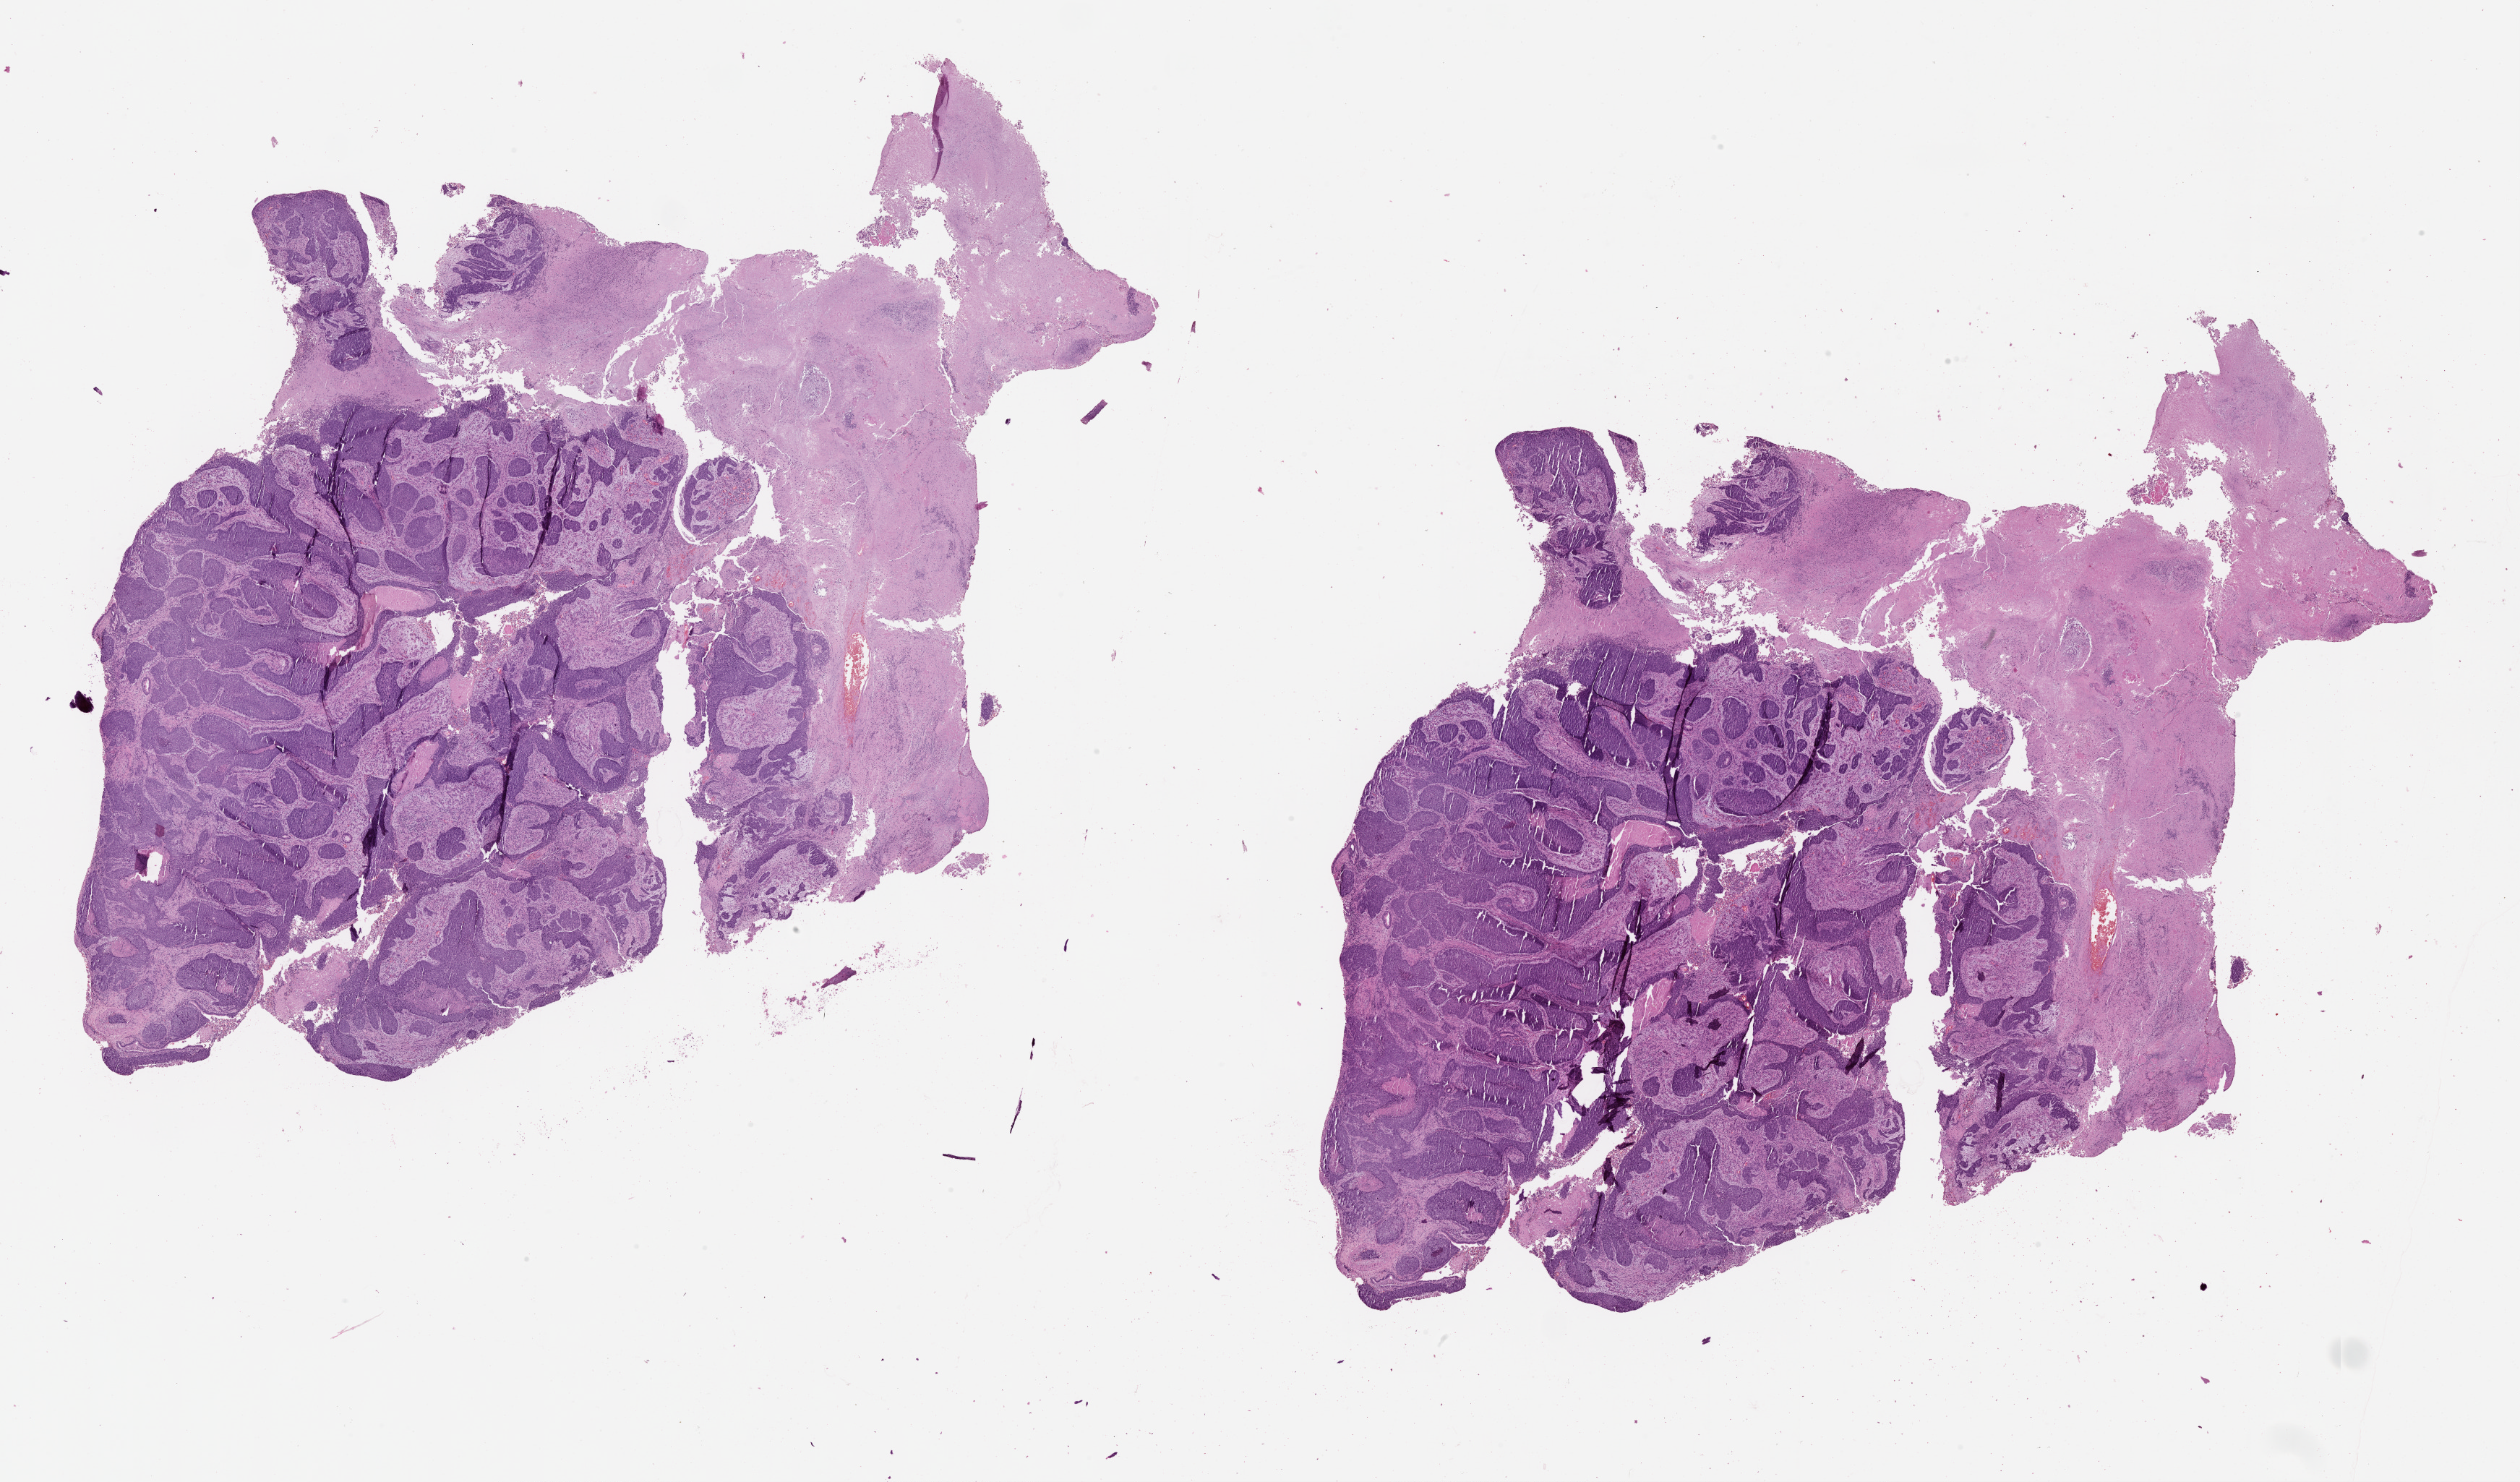
Hematoxylin and eosin (H&E) stained whole-slide image — whole scanned area (about 28.1 x 16.5 mm) shown as a low-resolution overview; tumour tissue sample, lung. Male, 59 y/o.
- patient diagnosis (cohort enrolment): squamous cell carcinoma (lung)